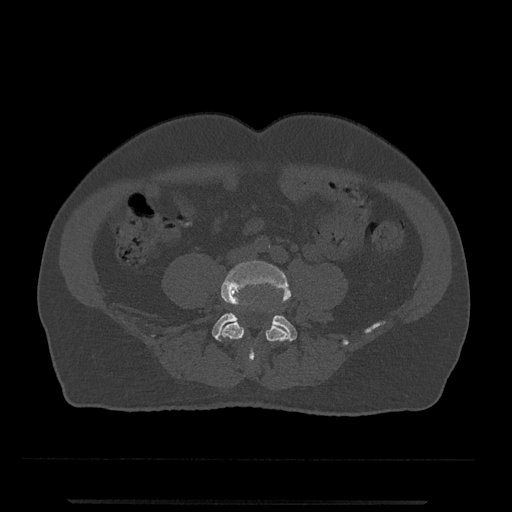
CT including the spine, one axial slice. Slice 106 of 797 in the series (ordered by position). Reconstruction kernel Br40s/3. 120 kVp. Bone window (W 1800 / L 400 HU). 0.5 mm slice thickness. 512 × 512 image matrix, field of view 419 × 419 mm. Patient: male, 63 years. From the clinical record (not read from this slice): primary cancer: prostate.
Annotated regions visible in this slice (semi-automatic segmentation, software-assisted and operator-edited):
- L4 vertebra: bounding box (x1, y1, x2, y2) in pixels: (220, 261, 293, 365)
- L5 vertebra: (212, 313, 297, 358)